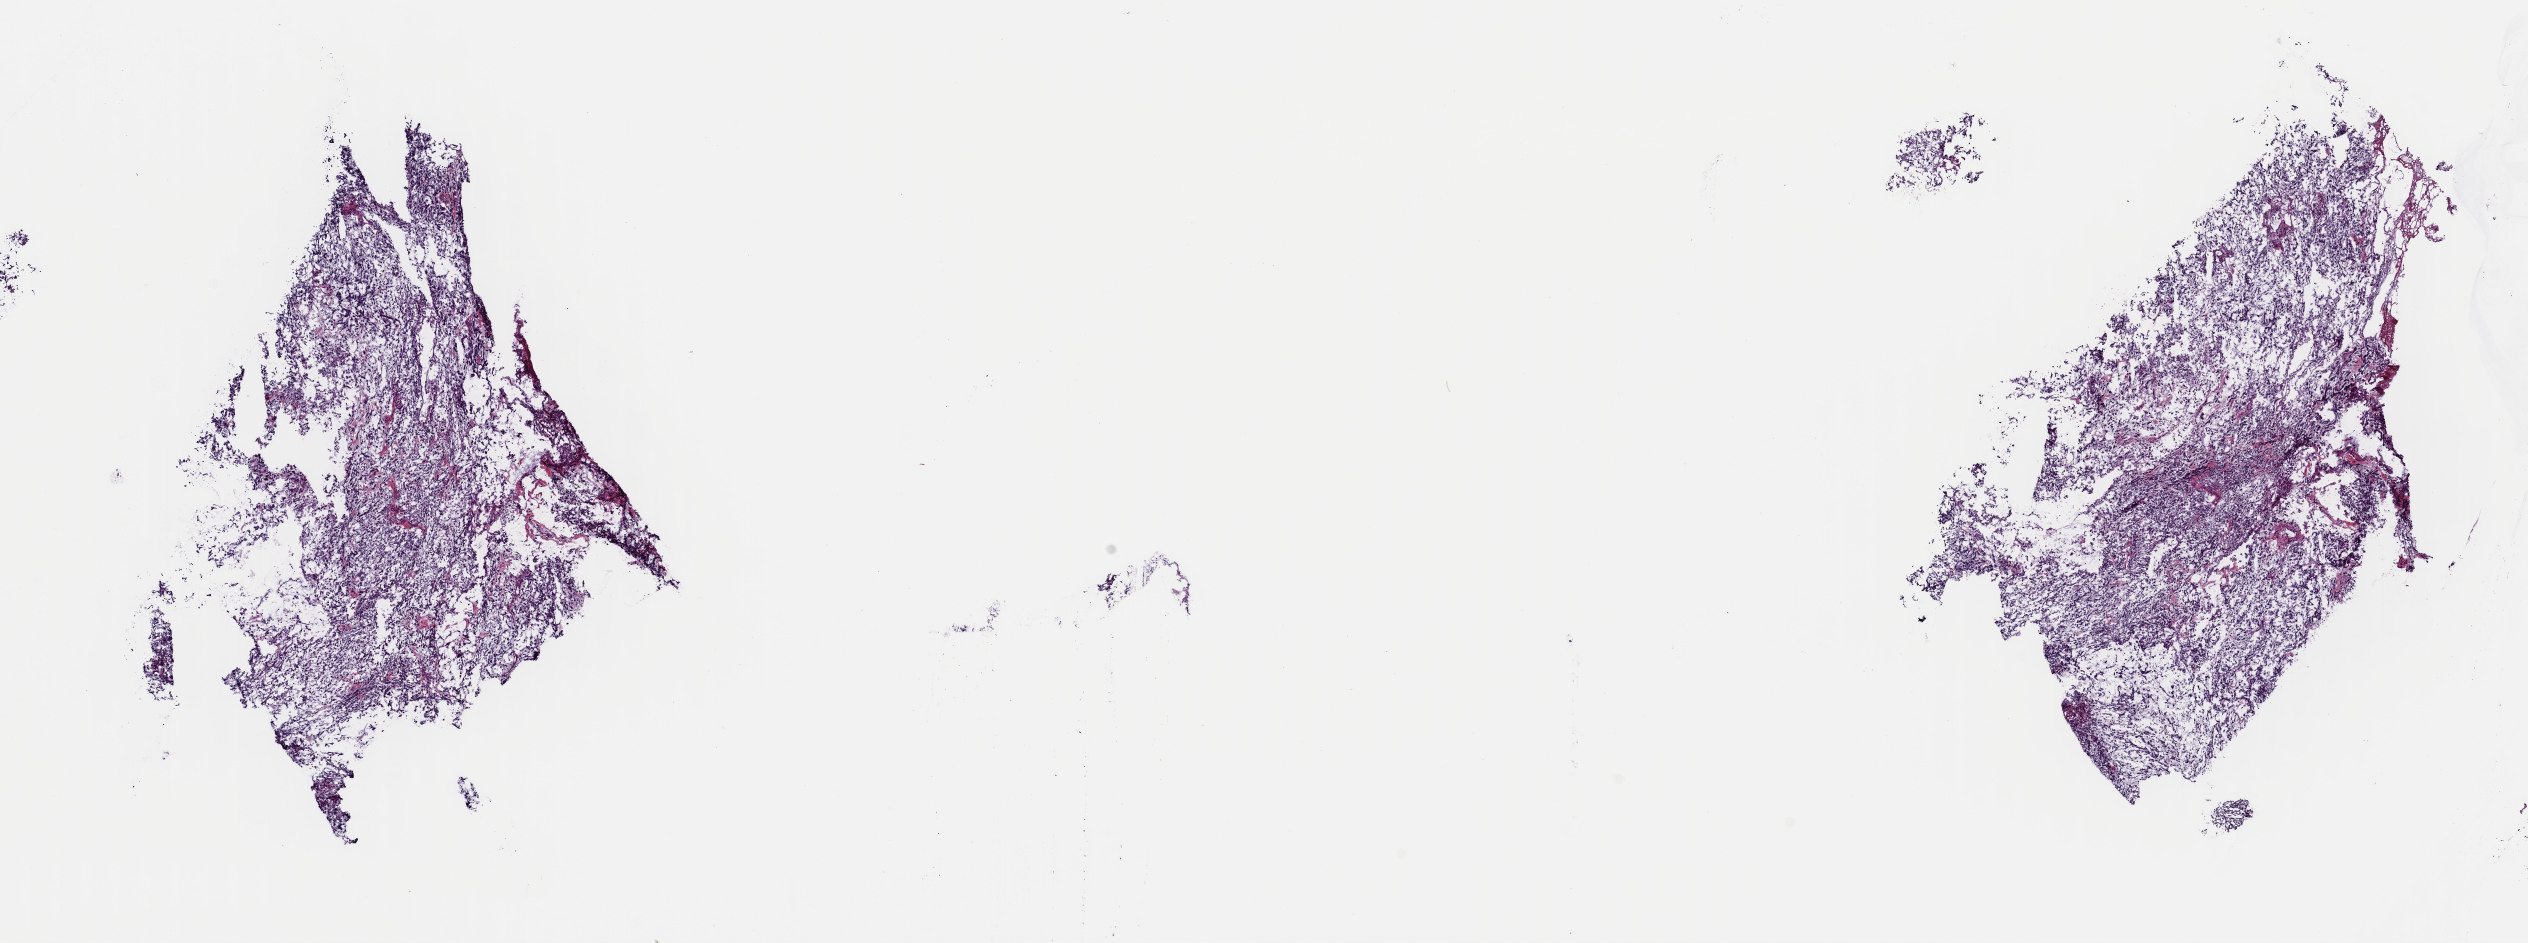
Hematoxylin and eosin (H&E) stained whole-slide image — whole scanned area (about 20.0 x 7.4 mm) shown as a low-resolution overview; frozen section from the top of the tissue portion; uterus, primary tumour sample. Patient: female, age at initial diagnosis 59 years. Slide review estimates, as recorded: tumour cells 90%, tumour nuclei 90%, normal cells 0%, stromal cells 10%, necrosis 0%. Inflammatory infiltration, as recorded: lymphocyte infiltration 0%, monocyte infiltration 0%, neutrophil infiltration 0%.
Pathologic diagnosis: Mullerian mixed tumor (endometrium). FIGO stage: IA.